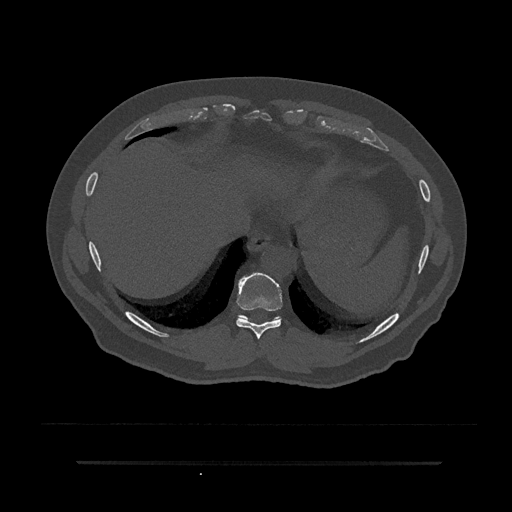
CT including the spine, one axial slice. Position 366 of 797 along the scan axis. Reconstruction kernel Br40s/3. Bone window (W 1800 / L 400 HU). 0.5 mm slice thickness. 512 × 512 image matrix. Patient: male, 59 years. Case-level facts recorded for this patient, not image findings: primary cancer: bile ducts.
Structures marked on this image (semi-automatically segmented with operator editing):
- T10 vertebra: box from (x=245, y=316) to (x=280, y=320) px
- T9 vertebra: (x=236, y=272)–(x=282, y=339)